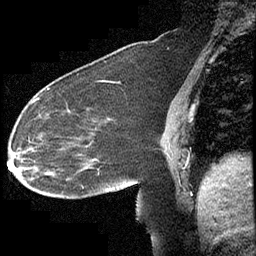
Breast MRI (dynamic contrast-enhanced), one sagittal slice. Position 157 of 232 along the scan axis. Dynamic contrast-enhanced study with each time point stored as its own series, time point 2 of 4 at this slice position (early post-contrast, ordered by acquisition time). 1.5 T. TE 4.2 ms, TR 6.7 ms. 3 mm slice thickness. 256 × 256 image matrix, field of view 200 × 200 mm. Patient: female, 63 years. Case-level facts recorded for this patient, not image findings: setting: breast cancer imaged before/during neoadjuvant chemotherapy; receptor status: triple-negative.
Outlined on this slice (semi-automatic segmentation, software-assisted and operator-edited):
- analysis volume of interest (the breast-tissue region the enhancement analysis was run in; not a lesion): bounding box (x1, y1, x2, y2) in pixels: (13, 90, 140, 211)
- tumour enhancement mask (voxels above the 70 % enhancement threshold inside the analysis volume of interest): (17, 98, 39, 169)